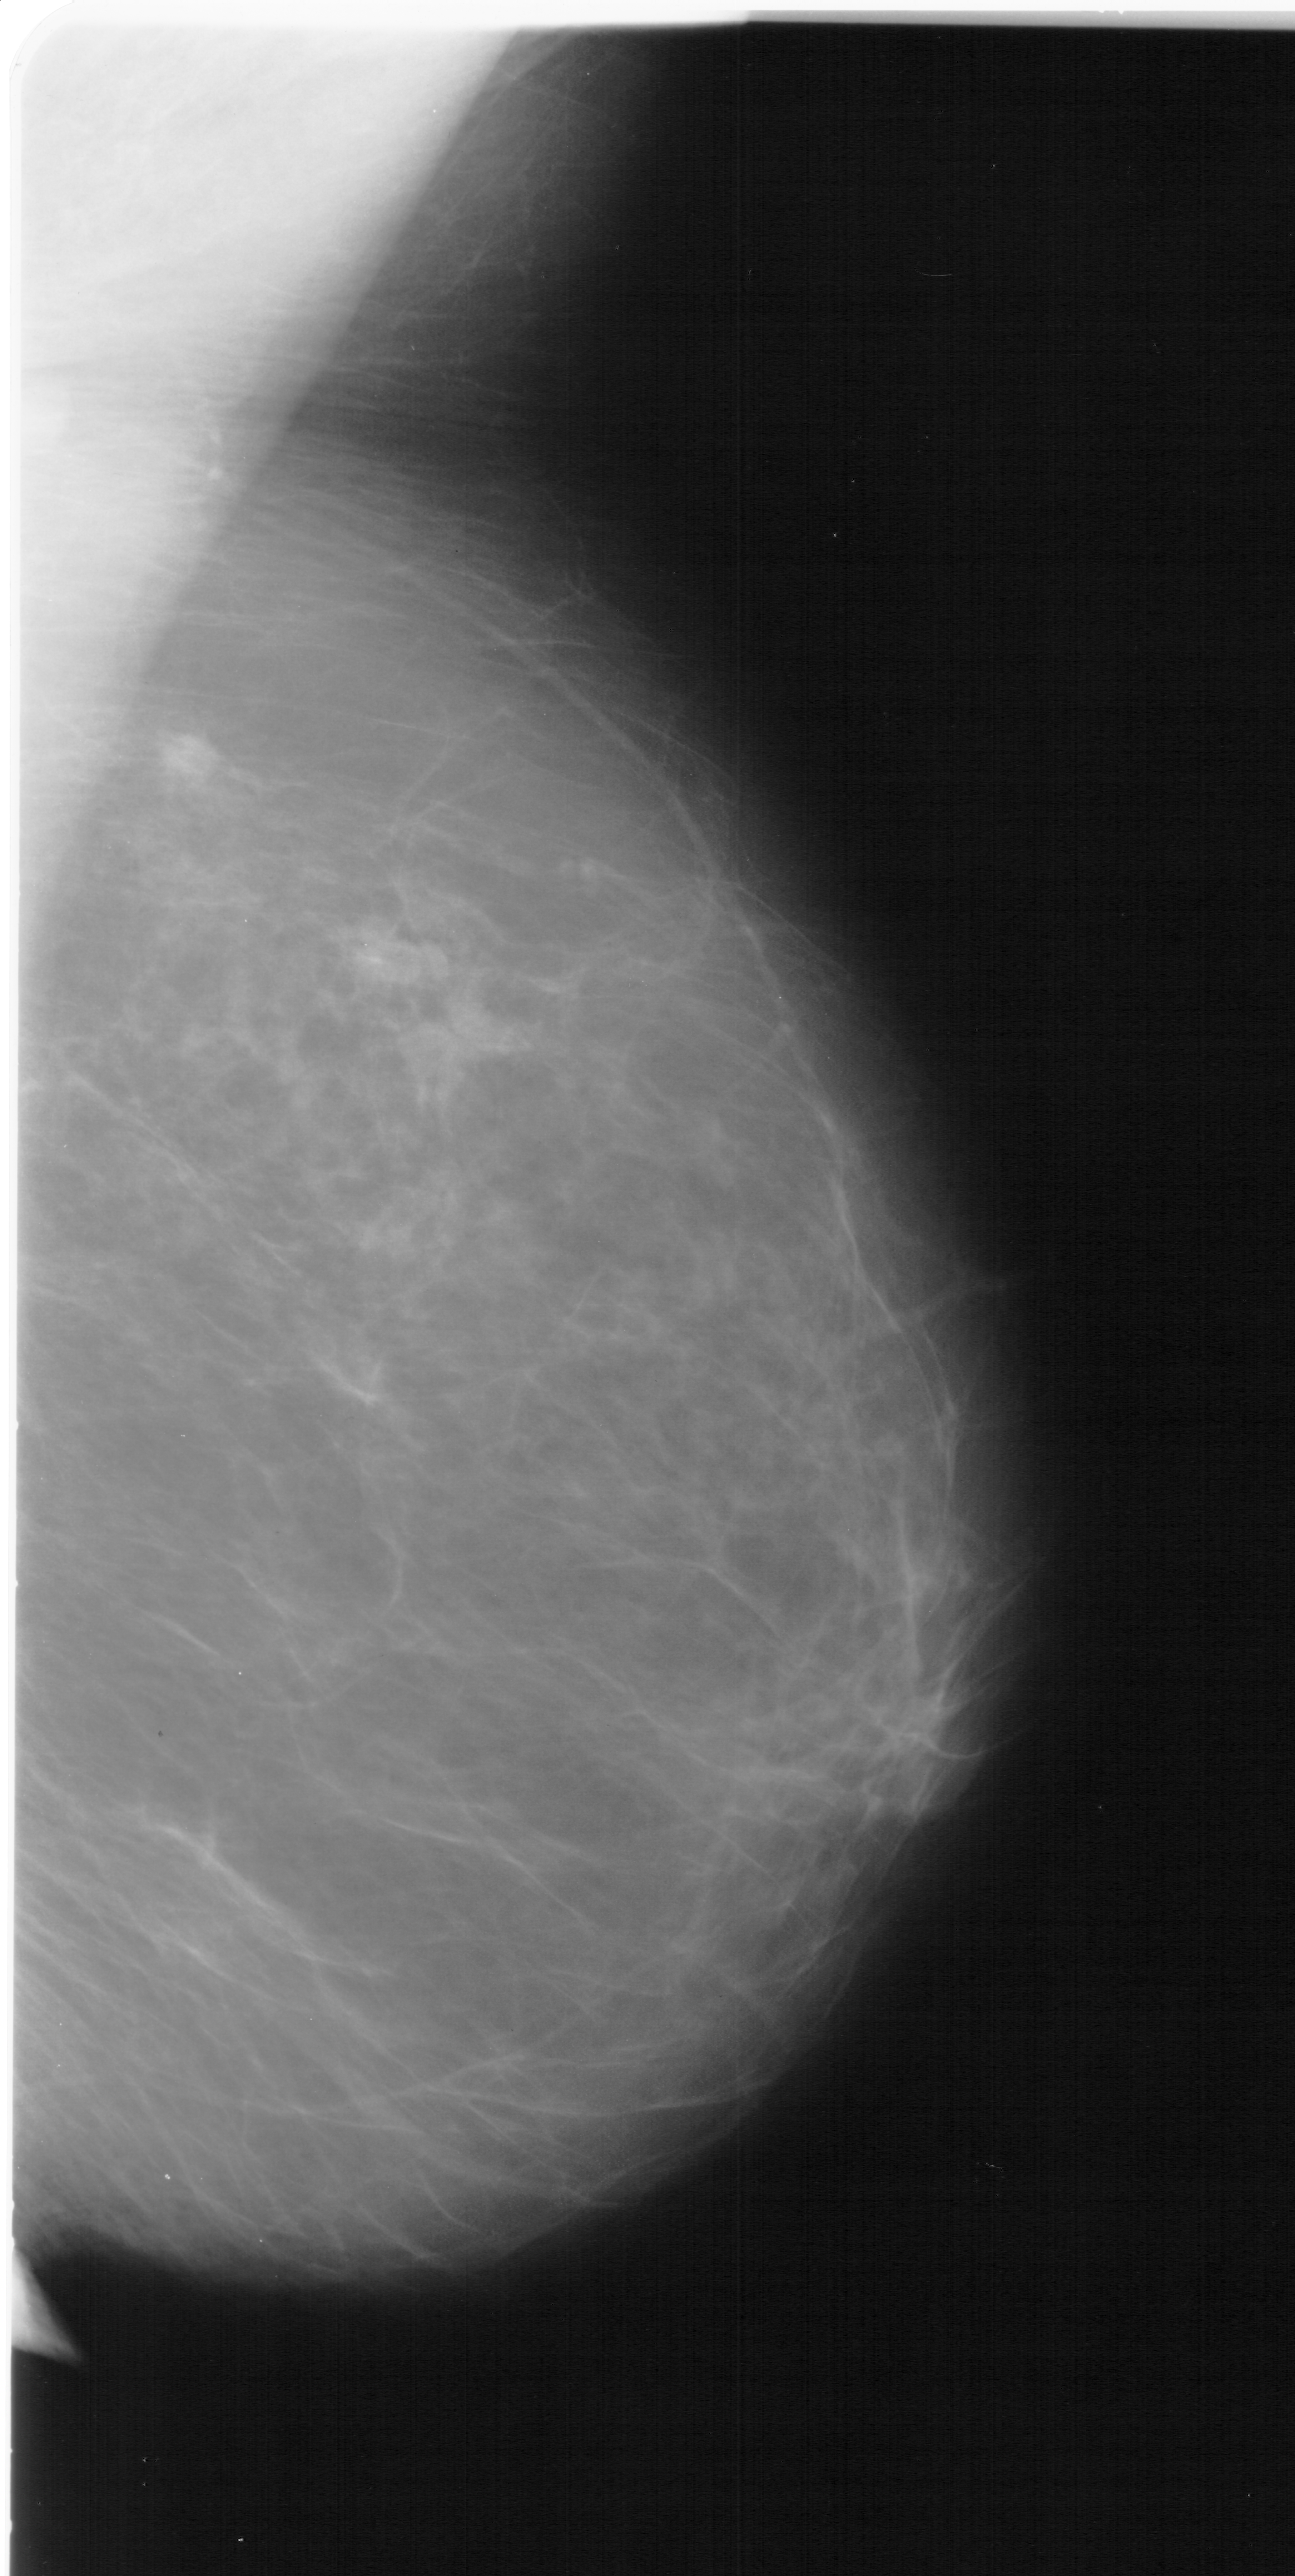
Digitized screen-film mammogram, right breast, MLO view, BI-RADS breast density category 2 (scale 1–4).
- Mass, shape irregular, margins ill defined; BI-RADS assessment category 4; subtlety rating 4 on a 1 (subtle) to 5 (obvious) scale; pathology (as recorded): malignant.